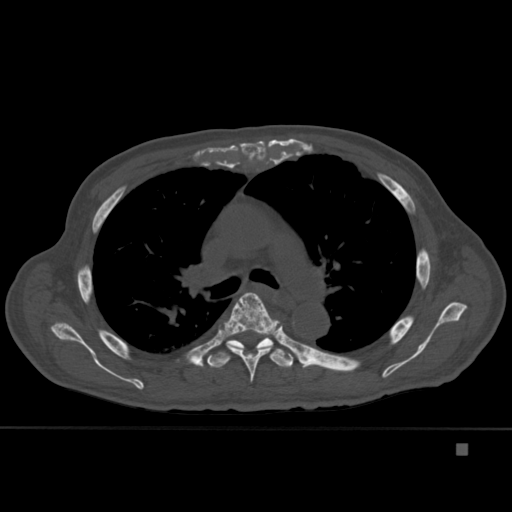
CT including the spine, one axial slice. Slice 303 of 451 in the series (ordered by position). Bone window (W 1800 / L 400 HU). 1.5 mm slice thickness. 512 × 512 image matrix. Male patient, age 75 years. Case-level facts recorded for this patient, not image findings: primary cancer: prostate.
Annotated regions visible in this slice (semi-automatically segmented with operator editing):
- T5 vertebra: bounding box <219,292,280,382> (left, top, right, bottom; pixels)
- T6 vertebra: <207,331,293,368>